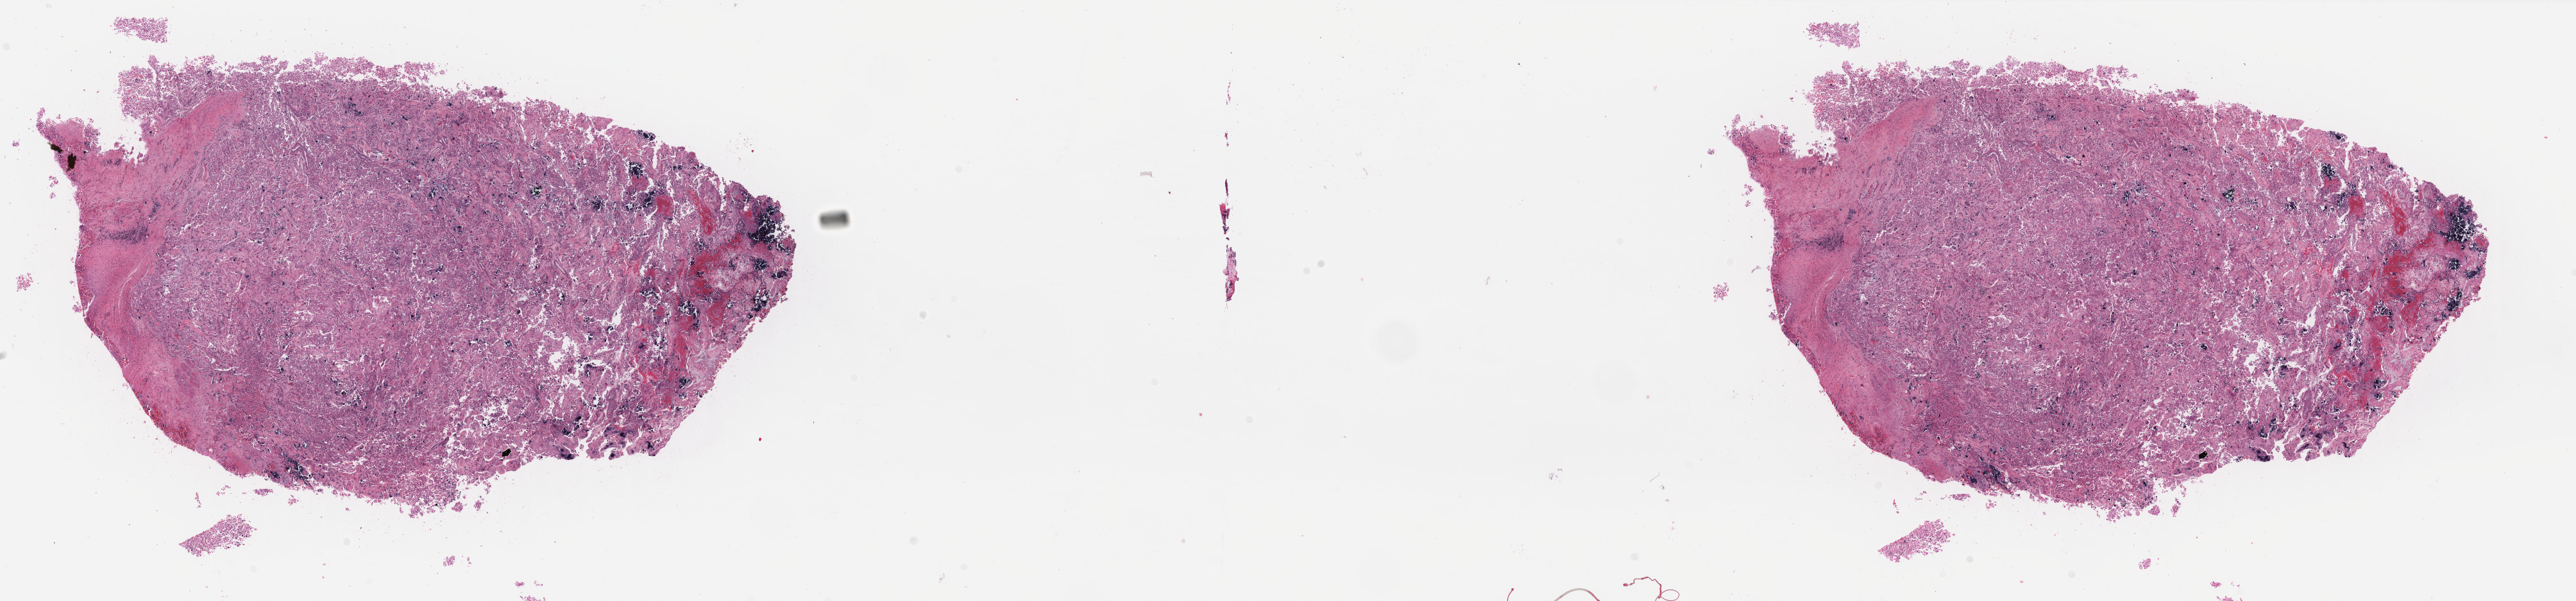
Whole-slide histology image, Hematoxylin and eosin (H&E) stained, a low-resolution overview of the entire scanned area, about 31.8 x 7.4 mm (slide scanned at 40x), formalin-fixed paraffin-embedded (FFPE) diagnostic section, primary tumour sample from the kidney. Male patient; age at initial diagnosis 56 years.
Laterality: left. TNM: T1b NX. Diagnosis: Renal cell carcinoma, chromophobe type. AJCC pathologic stage: I (7th edition).